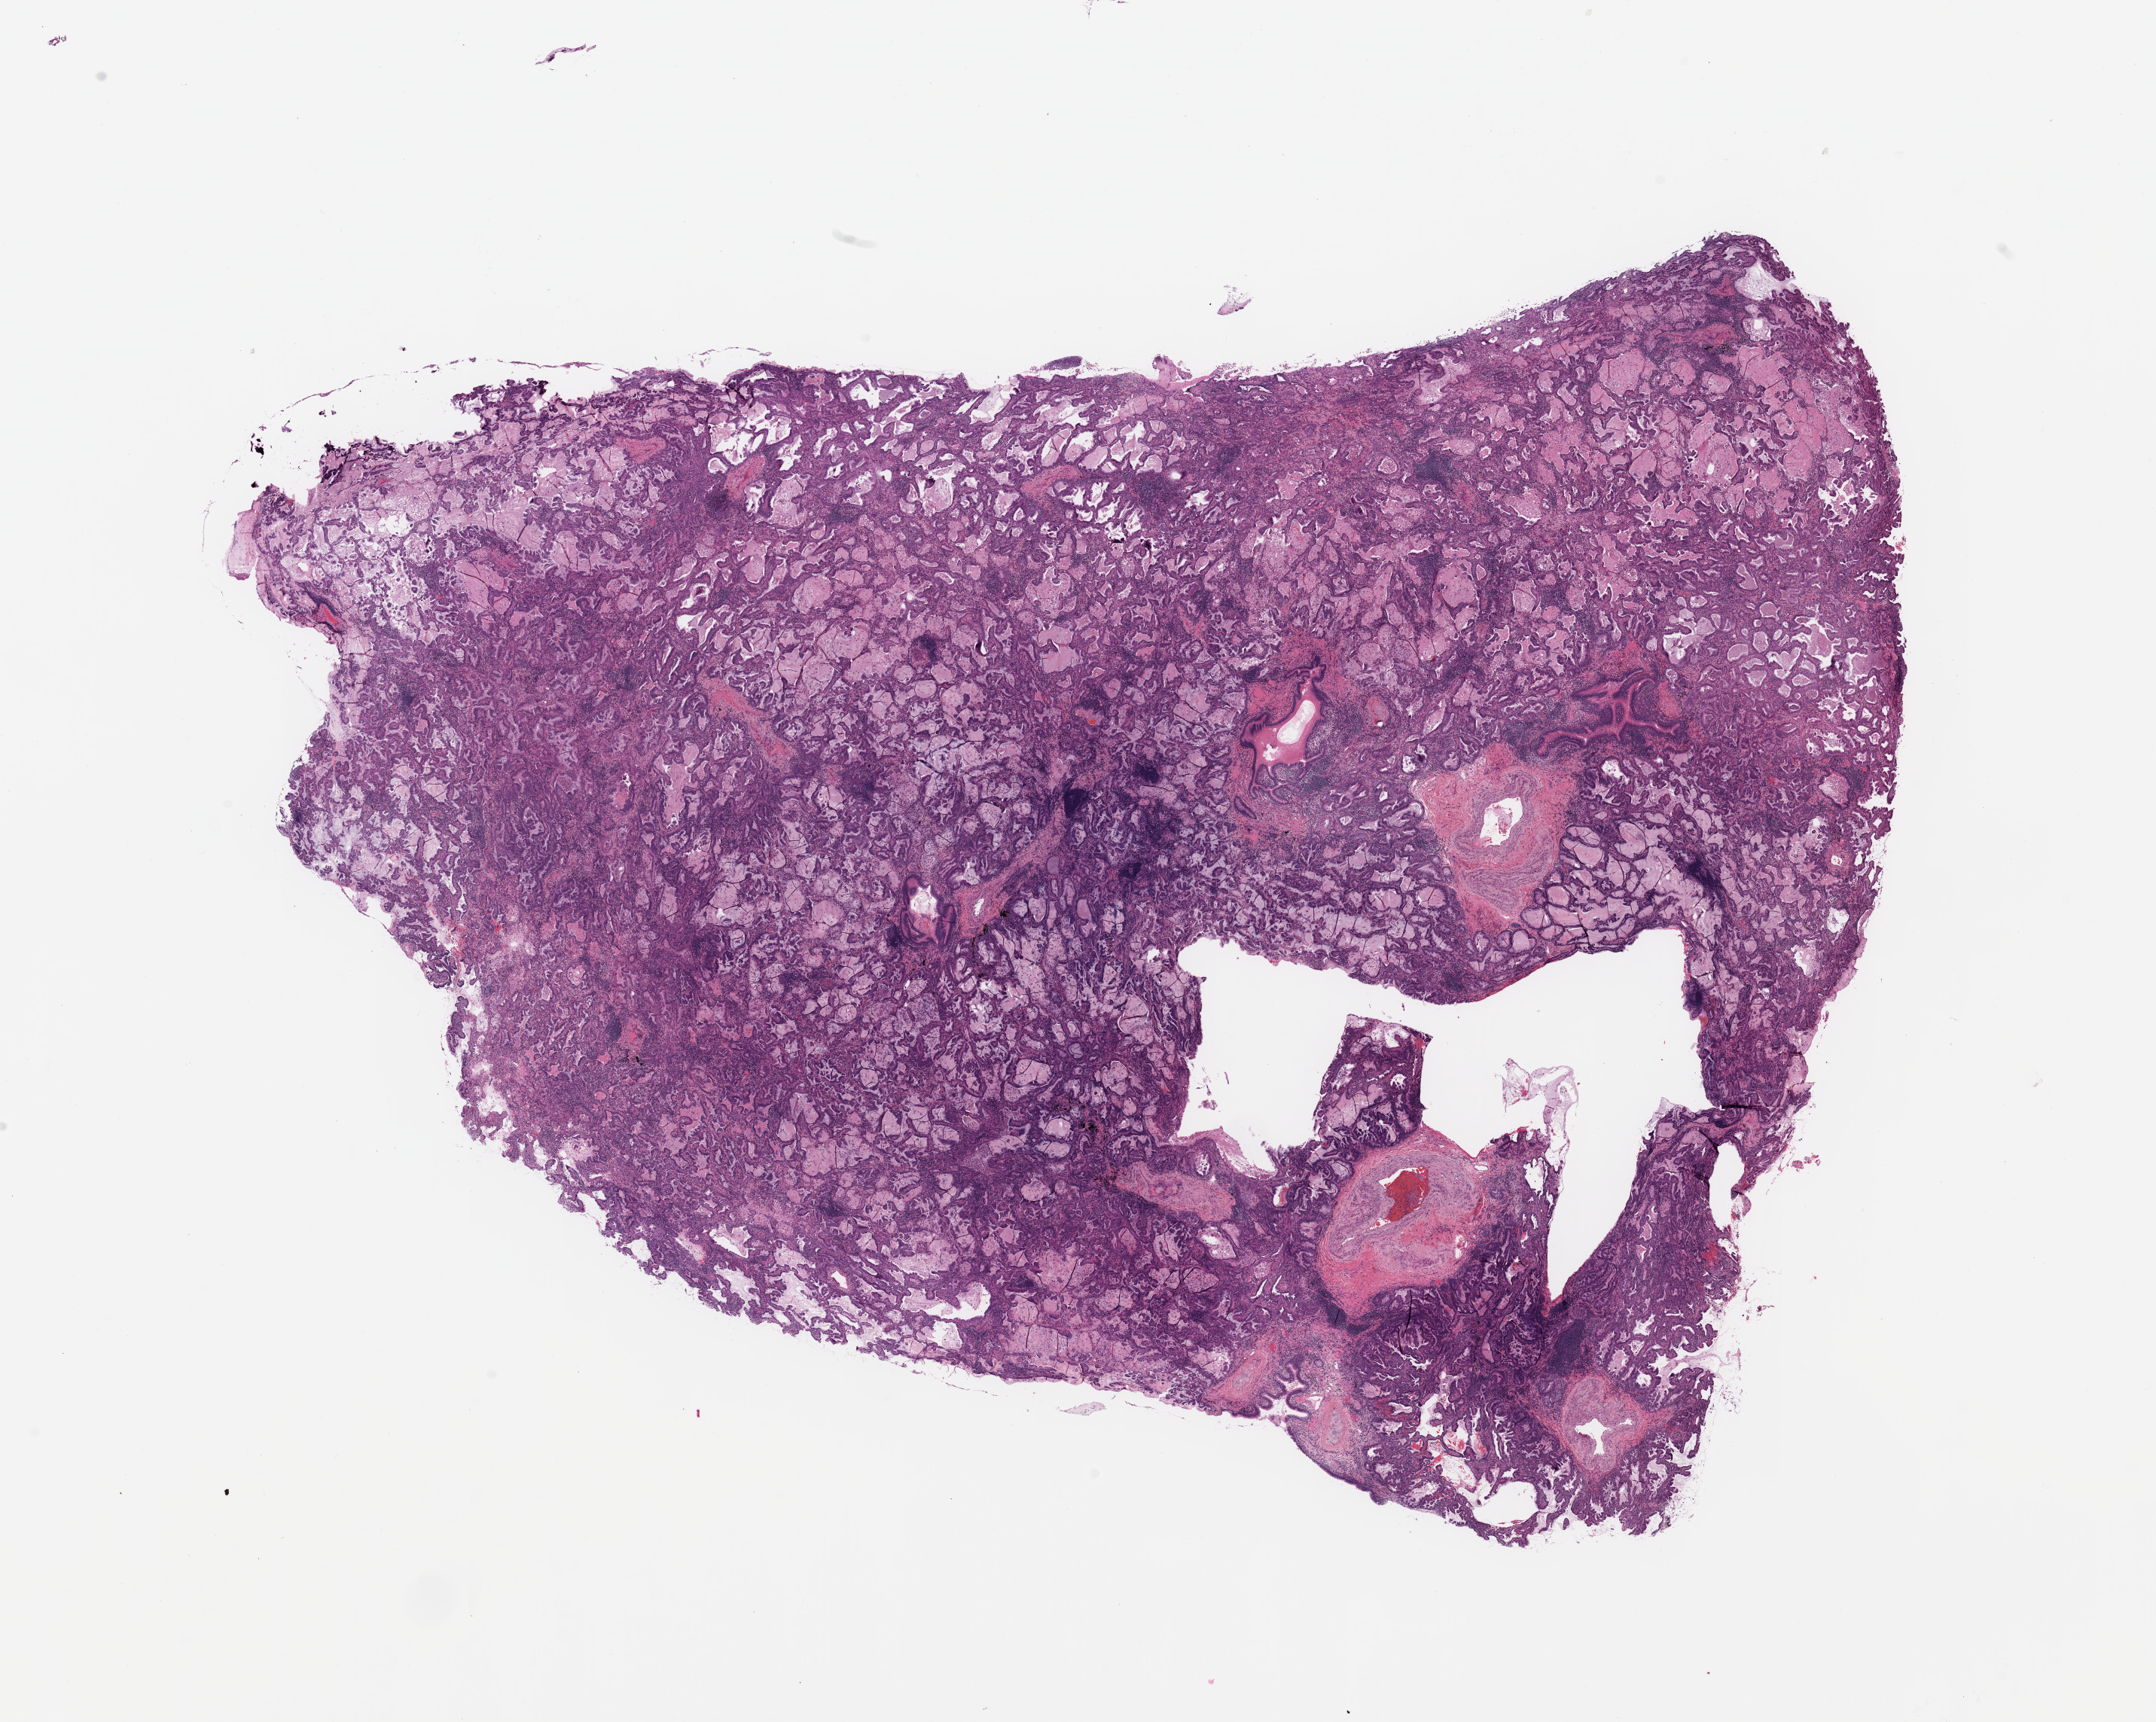
Digitized Hematoxylin and eosin (H&E) stained tissue section (whole slide) — a low-resolution overview of the entire scanned area, about 22.6 x 18.1 mm (from a 20x scan). Tumour tissue sample, sampled site: lung. 76-year-old male patient. Histologic grade: G2 (moderately differentiated). Pathologist review of this section (percent, as recorded): tumour nuclei 70%, necrosis 5%.
Primary tumour site (as recorded): right lower lobe. AJCC pathologic stage: IB. Histologic diagnosis: Adenocarcinoma, NOS.